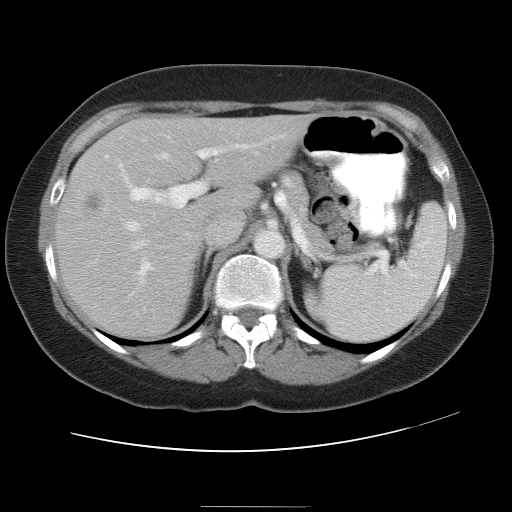
Contrast-enhanced abdominal CT, one axial slice; position 21 of 30 along the scan axis; intravenous contrast given; soft-tissue window (W 400 / L 40 HU); 7.5 mm slice thickness; 512 × 512 image matrix, field of view 376 × 376 mm. Female patient, age 52 years. Case-level facts recorded for this patient, not image findings: diagnosis: colorectal cancer liver metastases, imaged before liver resection; multiple liver metastases: no; largest metastasis: 3 cm; chemotherapy before resection: yes.
Structures marked on this image (expert manual segmentation):
- hepatic veins: bounding box [x1, y1, x2, y2] px = [125, 153, 167, 249]
- liver: [55, 116, 307, 336]
- planned liver remnant (the part of the liver to remain after resection): [148, 116, 307, 207]
- portal vein (with intrahepatic branches): [121, 140, 268, 285]
- liver metastasis: [86, 196, 104, 210]